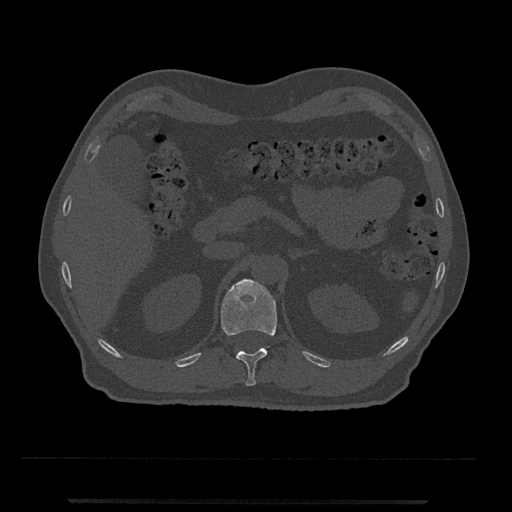
CT including the spine, one axial slice. Position 388 of 797 along the scan axis. Reconstruction kernel Br40s/3. 120 kVp. Bone window (W 1800 / L 400 HU). 0.5 mm slice thickness. 512 × 512 image matrix, field of view 419 × 419 mm. Male patient, age 63 years. From the clinical record (not read from this slice): primary cancer: prostate.
Annotated regions visible in this slice (semi-automatically segmented with operator editing):
- T12 vertebra: bounding box (x1, y1, x2, y2) in pixels: (221, 279, 278, 386)